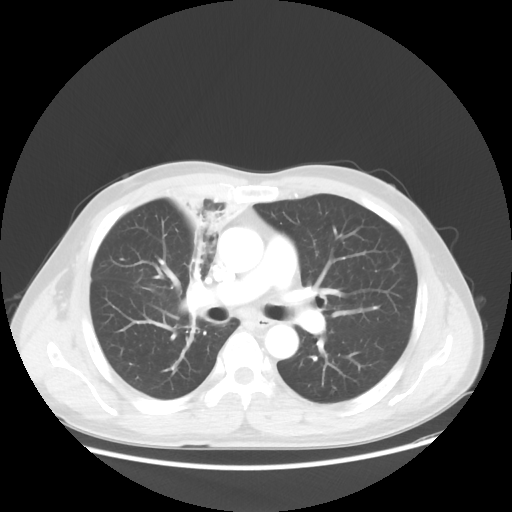
Chest CT, one axial slice; position 32 of 56 along the scan axis; reconstruction kernel STANDARD; 100 kVp; lung window (W 1500 / L -600 HU); 512 × 512 image matrix. Patient: male, 60 years. Case-level facts recorded for this patient, not image findings: clinical TNM (as recorded): T2a N1 M0.
Annotated regions visible in this slice (bounding box drawn by a radiologist):
- lung tumour (recorded histology: squamous cell carcinoma): bounding box <168,167,246,274> (left, top, right, bottom; pixels)